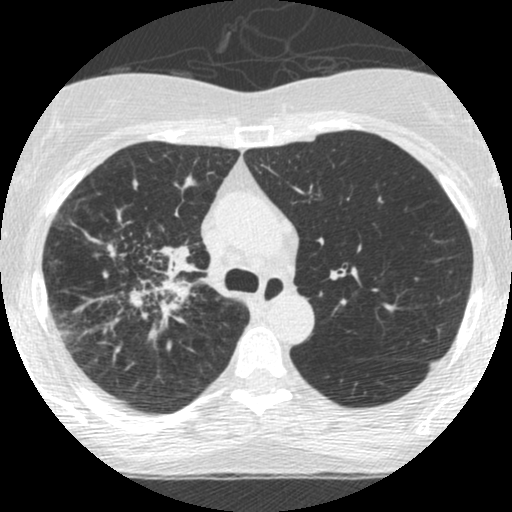
Low-dose screening chest CT, one axial slice. Slice 180 of 253 in the series (ordered by position). Reconstruction kernel STANDARD. Lung window (W 1500 / L -600 HU). 512 × 512 image matrix, field of view 294 × 294 mm.
Annotated regions visible in this slice (manually delineated by an expert):
- lesion 2 (tumor, hilum of right lung): bounding box (x1, y1, x2, y2) in pixels: (125, 245, 199, 343)